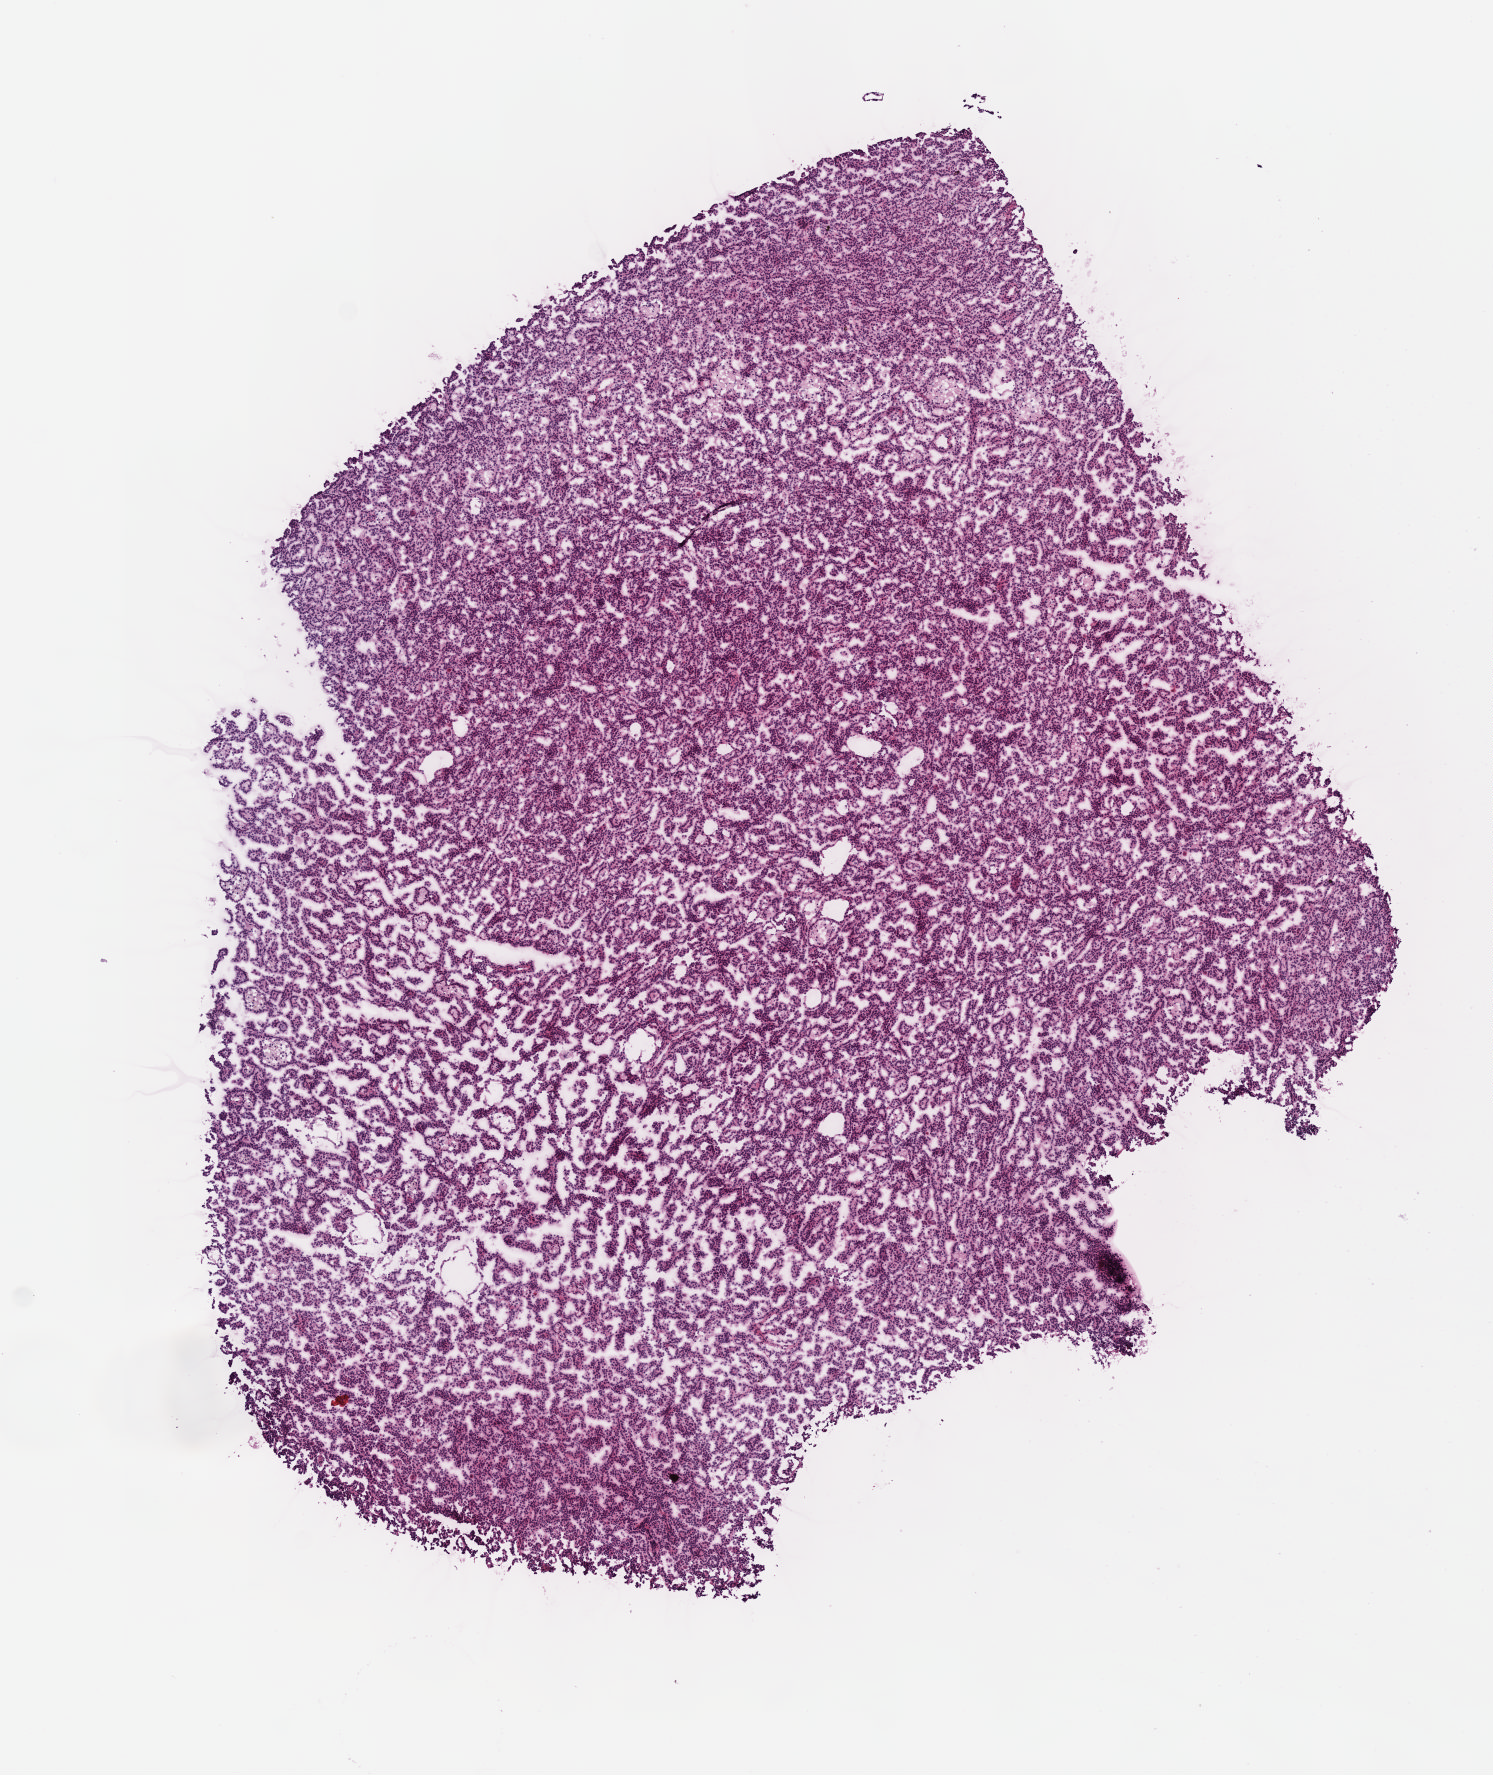
Whole-slide histology image, H&E — whole scanned area (about 6.0 x 7.2 mm, from a 40x scan) shown as a low-resolution overview. Formalin-fixed paraffin-embedded (FFPE) diagnostic section. Sample: primary tumour, kidney. Male, age 47 years at initial diagnosis.
AJCC pathologic stage: I (7th edition). Diagnosis: Papillary adenocarcinoma, NOS.